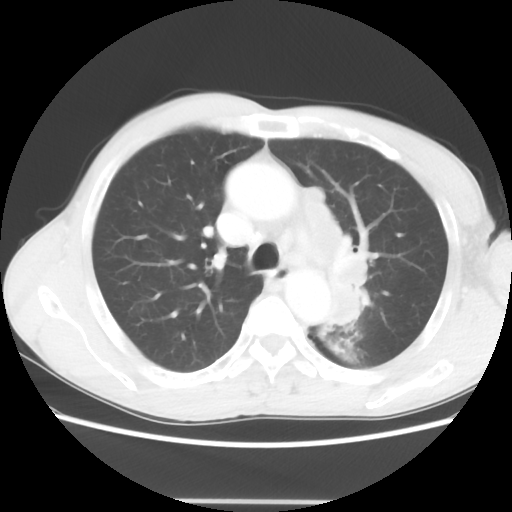
Chest CT, one axial slice; position 44 of 62 along the scan axis; reconstruction kernel STANDARD; 100 kVp; lung window (W 1500 / L -600 HU); 512 × 512 image matrix, field of view 360 × 360 mm. Patient: male, 61 years. From the clinical record (not read from this slice): clinical TNM (as recorded): T3 N1 M1.
Annotated regions visible in this slice (bounding box drawn by a radiologist):
- lung tumour (recorded histology: adenocarcinoma): bounding box [x1, y1, x2, y2] px = [303, 189, 375, 336]